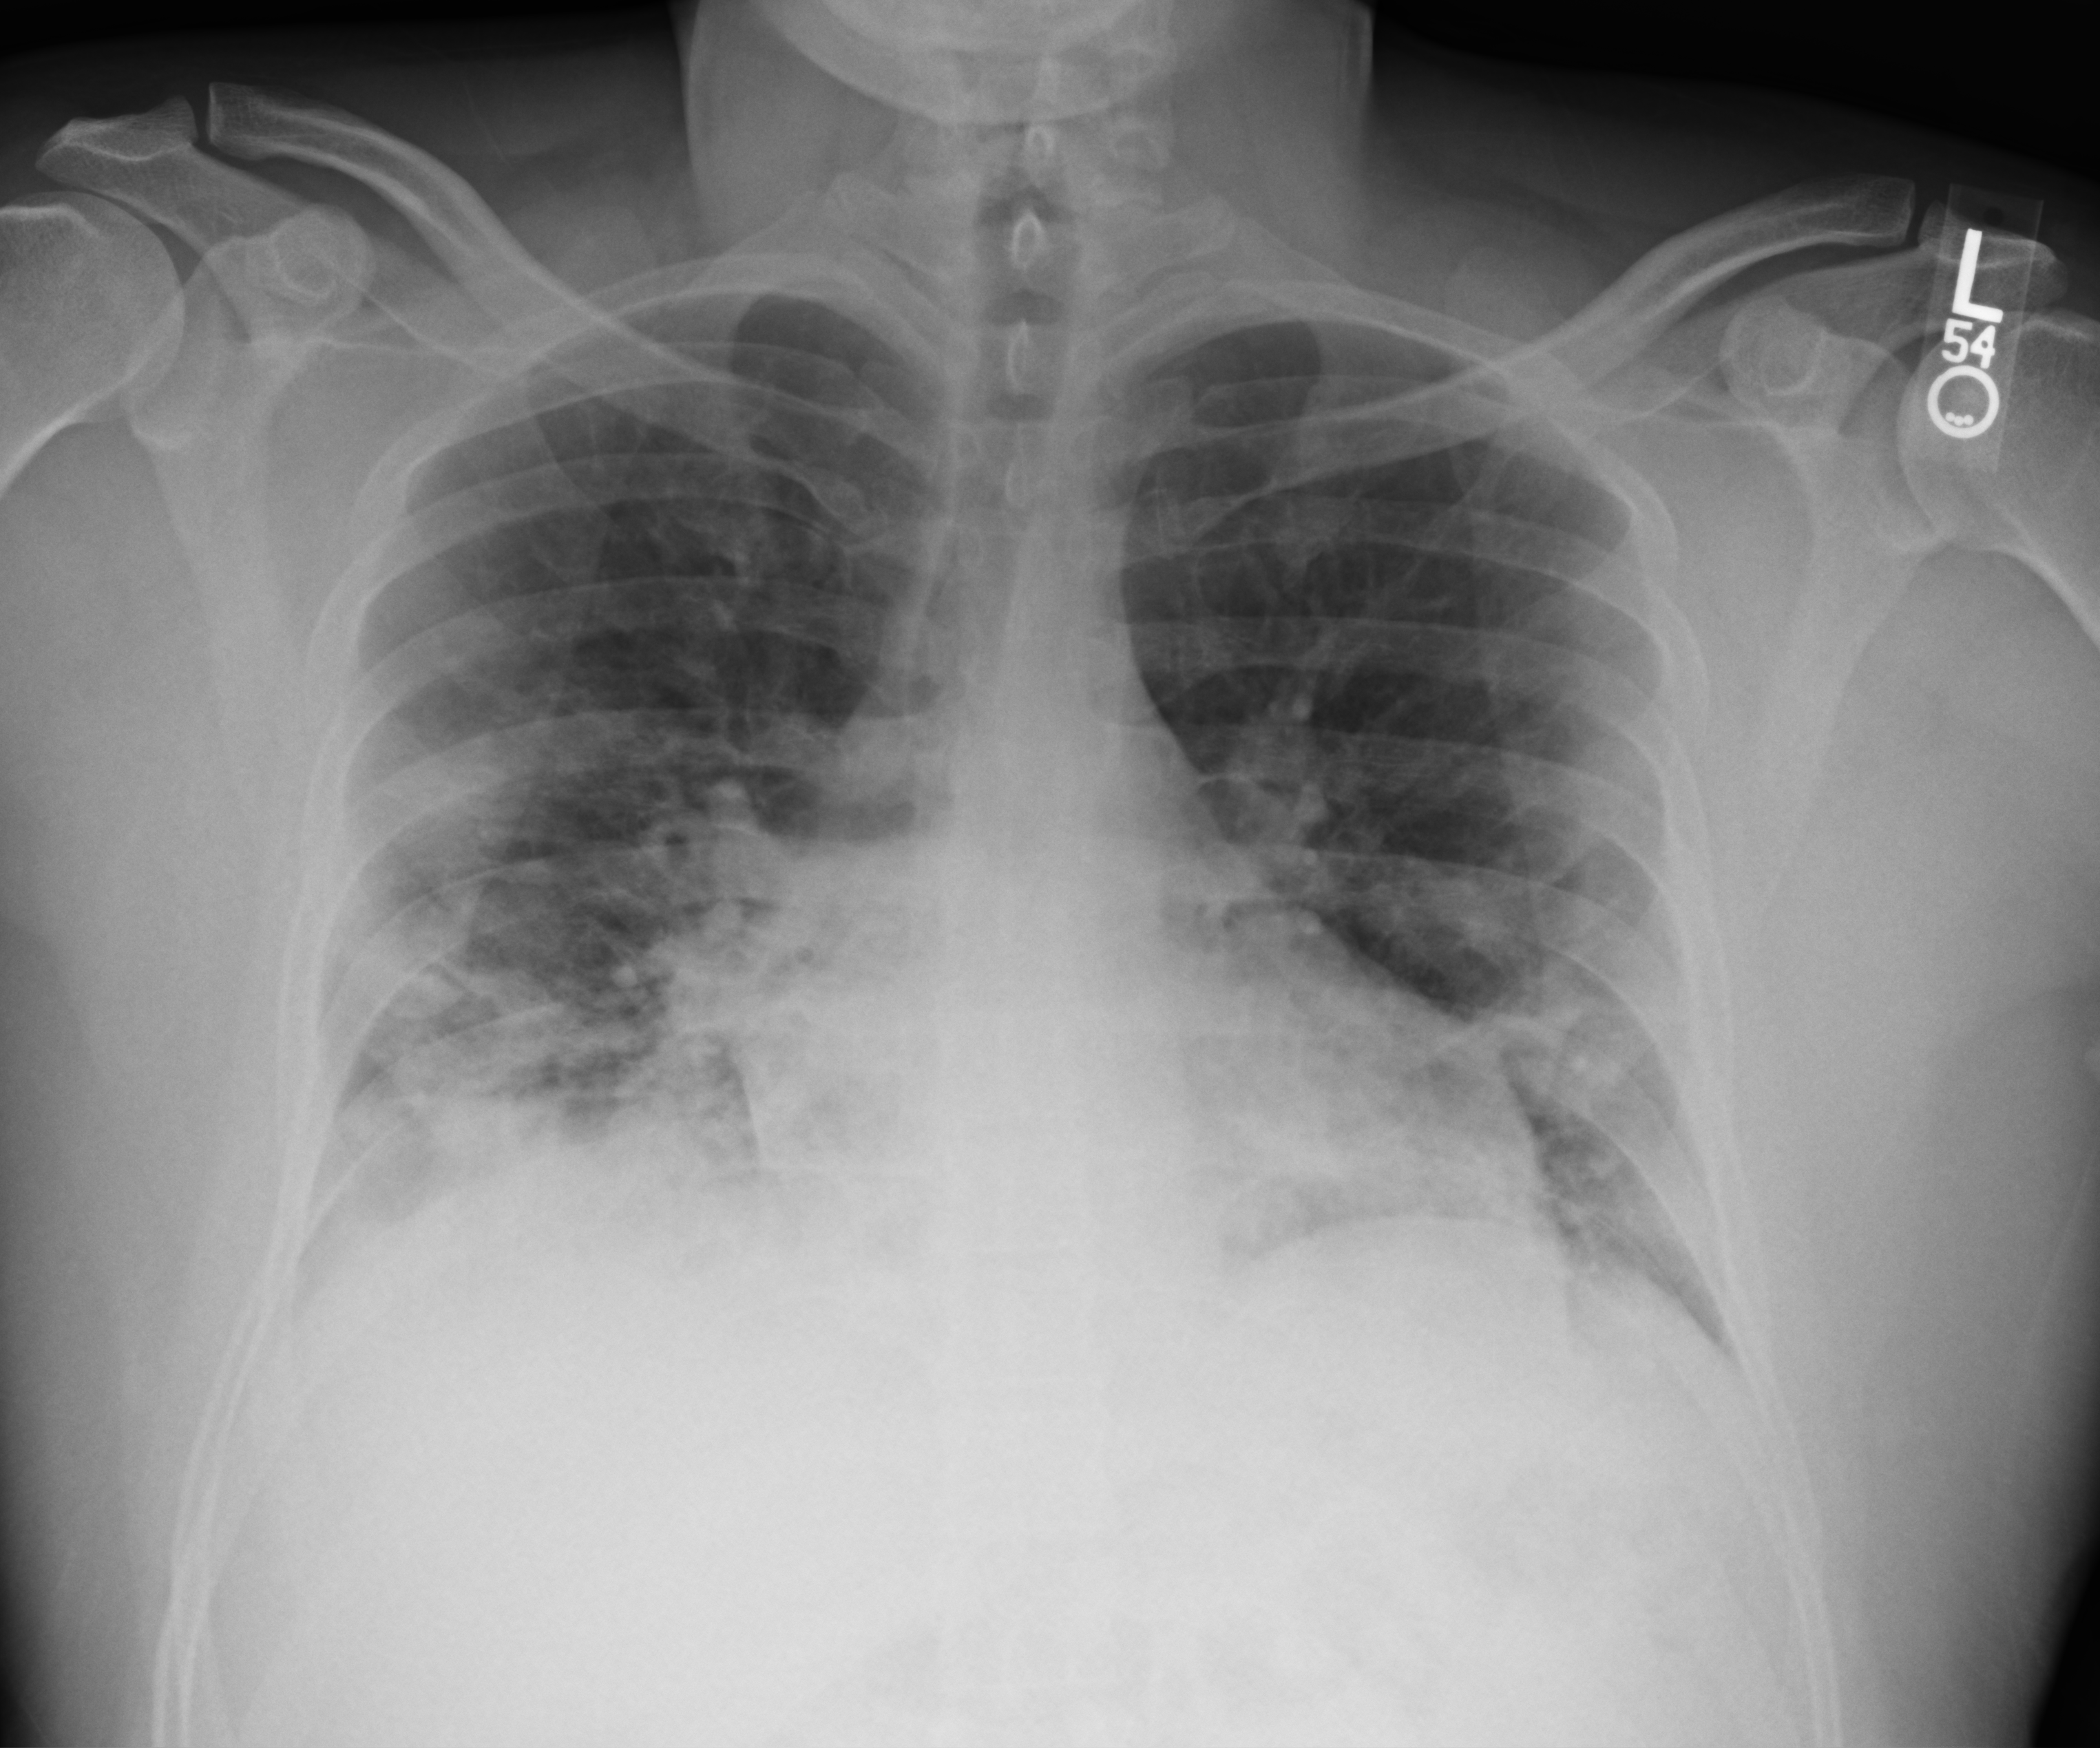
Chest X-ray (portable), anteroposterior (AP) projection. Male patient hospitalised with COVID-19, age 18–59 years.
Admission-level facts for this patient (not findings on this image; timing relative to this image not recorded): diabetes (admission record): no; admitted to intensive care during this hospital stay: yes; COPD (admission record): no.